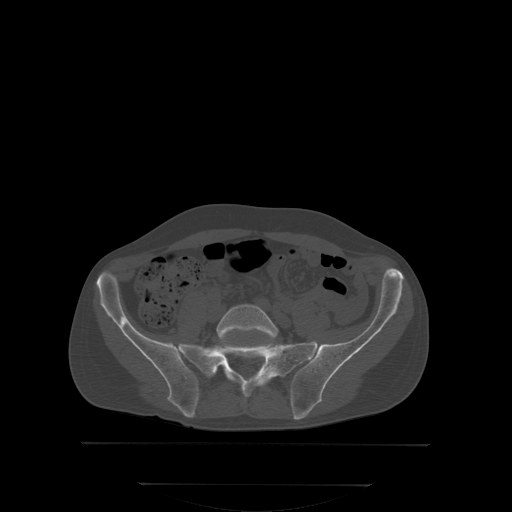
CT including the spine, one axial slice; position 88 of 350 along the scan axis; bone window (W 1800 / L 400 HU); 512 × 512 image matrix, field of view 500 × 500 mm. Patient: male, 58 years. From the clinical record (not read from this slice): primary cancer: prostate.
Outlined on this slice (semi-automatically segmented with operator editing):
- L5 vertebra: bounding box [x1, y1, x2, y2] px = [216, 304, 278, 340]